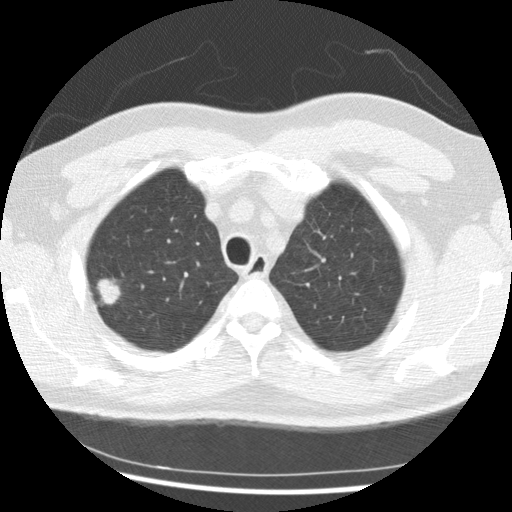
Axial slice from a low-dose chest CT screening exam, first (baseline) screen, lung window (W 1500 / L -600 HU), 2.5 mm slice thickness, standard (soft-tissue) reconstruction kernel (STANDARD), slice 51 of 265 in the series, 512 × 512 image matrix. Male, age 56 years at enrolment.
• Expert reader's lesion annotation, bounding box <83,273,132,315> (left, top, right, bottom; pixels).
• The exam's reader record, not a measurement of the box and not confirmed to be the same lesion: non-calcified nodule or mass ≥4 mm, right upper lobe, 19 × 15 mm, spiculated (stellate) margins, soft tissue attenuation.
• Official screen result: positive, change unspecified: nodule(s) >= 4 mm or enlarging nodule(s), mass(es), or other non-specific abnormalities suspicious for lung cancer.
• Lung cancer was diagnosed 291 days after this screen: non-small cell carcinoma, right upper lobe, poorly differentiated (G3), stage IIIB (AJCC 6th edition), 20 mm at pathology.